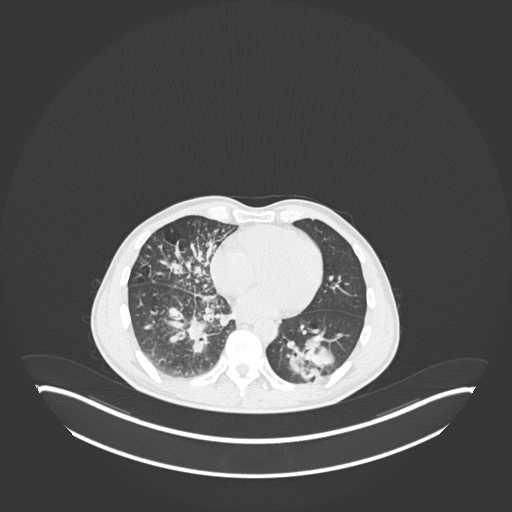
Chest CT, one axial slice. Position 89 of 237 along the scan axis. Reconstruction kernel B30f. Lung window (W 1500 / L -600 HU). 512 × 512 image matrix, field of view 500 × 500 mm. Patient: male, 49 years. Case-level facts recorded for this patient, not image findings: clinical TNM (as recorded): T2b N1 M0.
Outlined on this slice (rectangle marked by the reading radiologist):
- lung tumour (recorded histology: adenocarcinoma): bounding box [x1, y1, x2, y2] px = [283, 325, 341, 384]